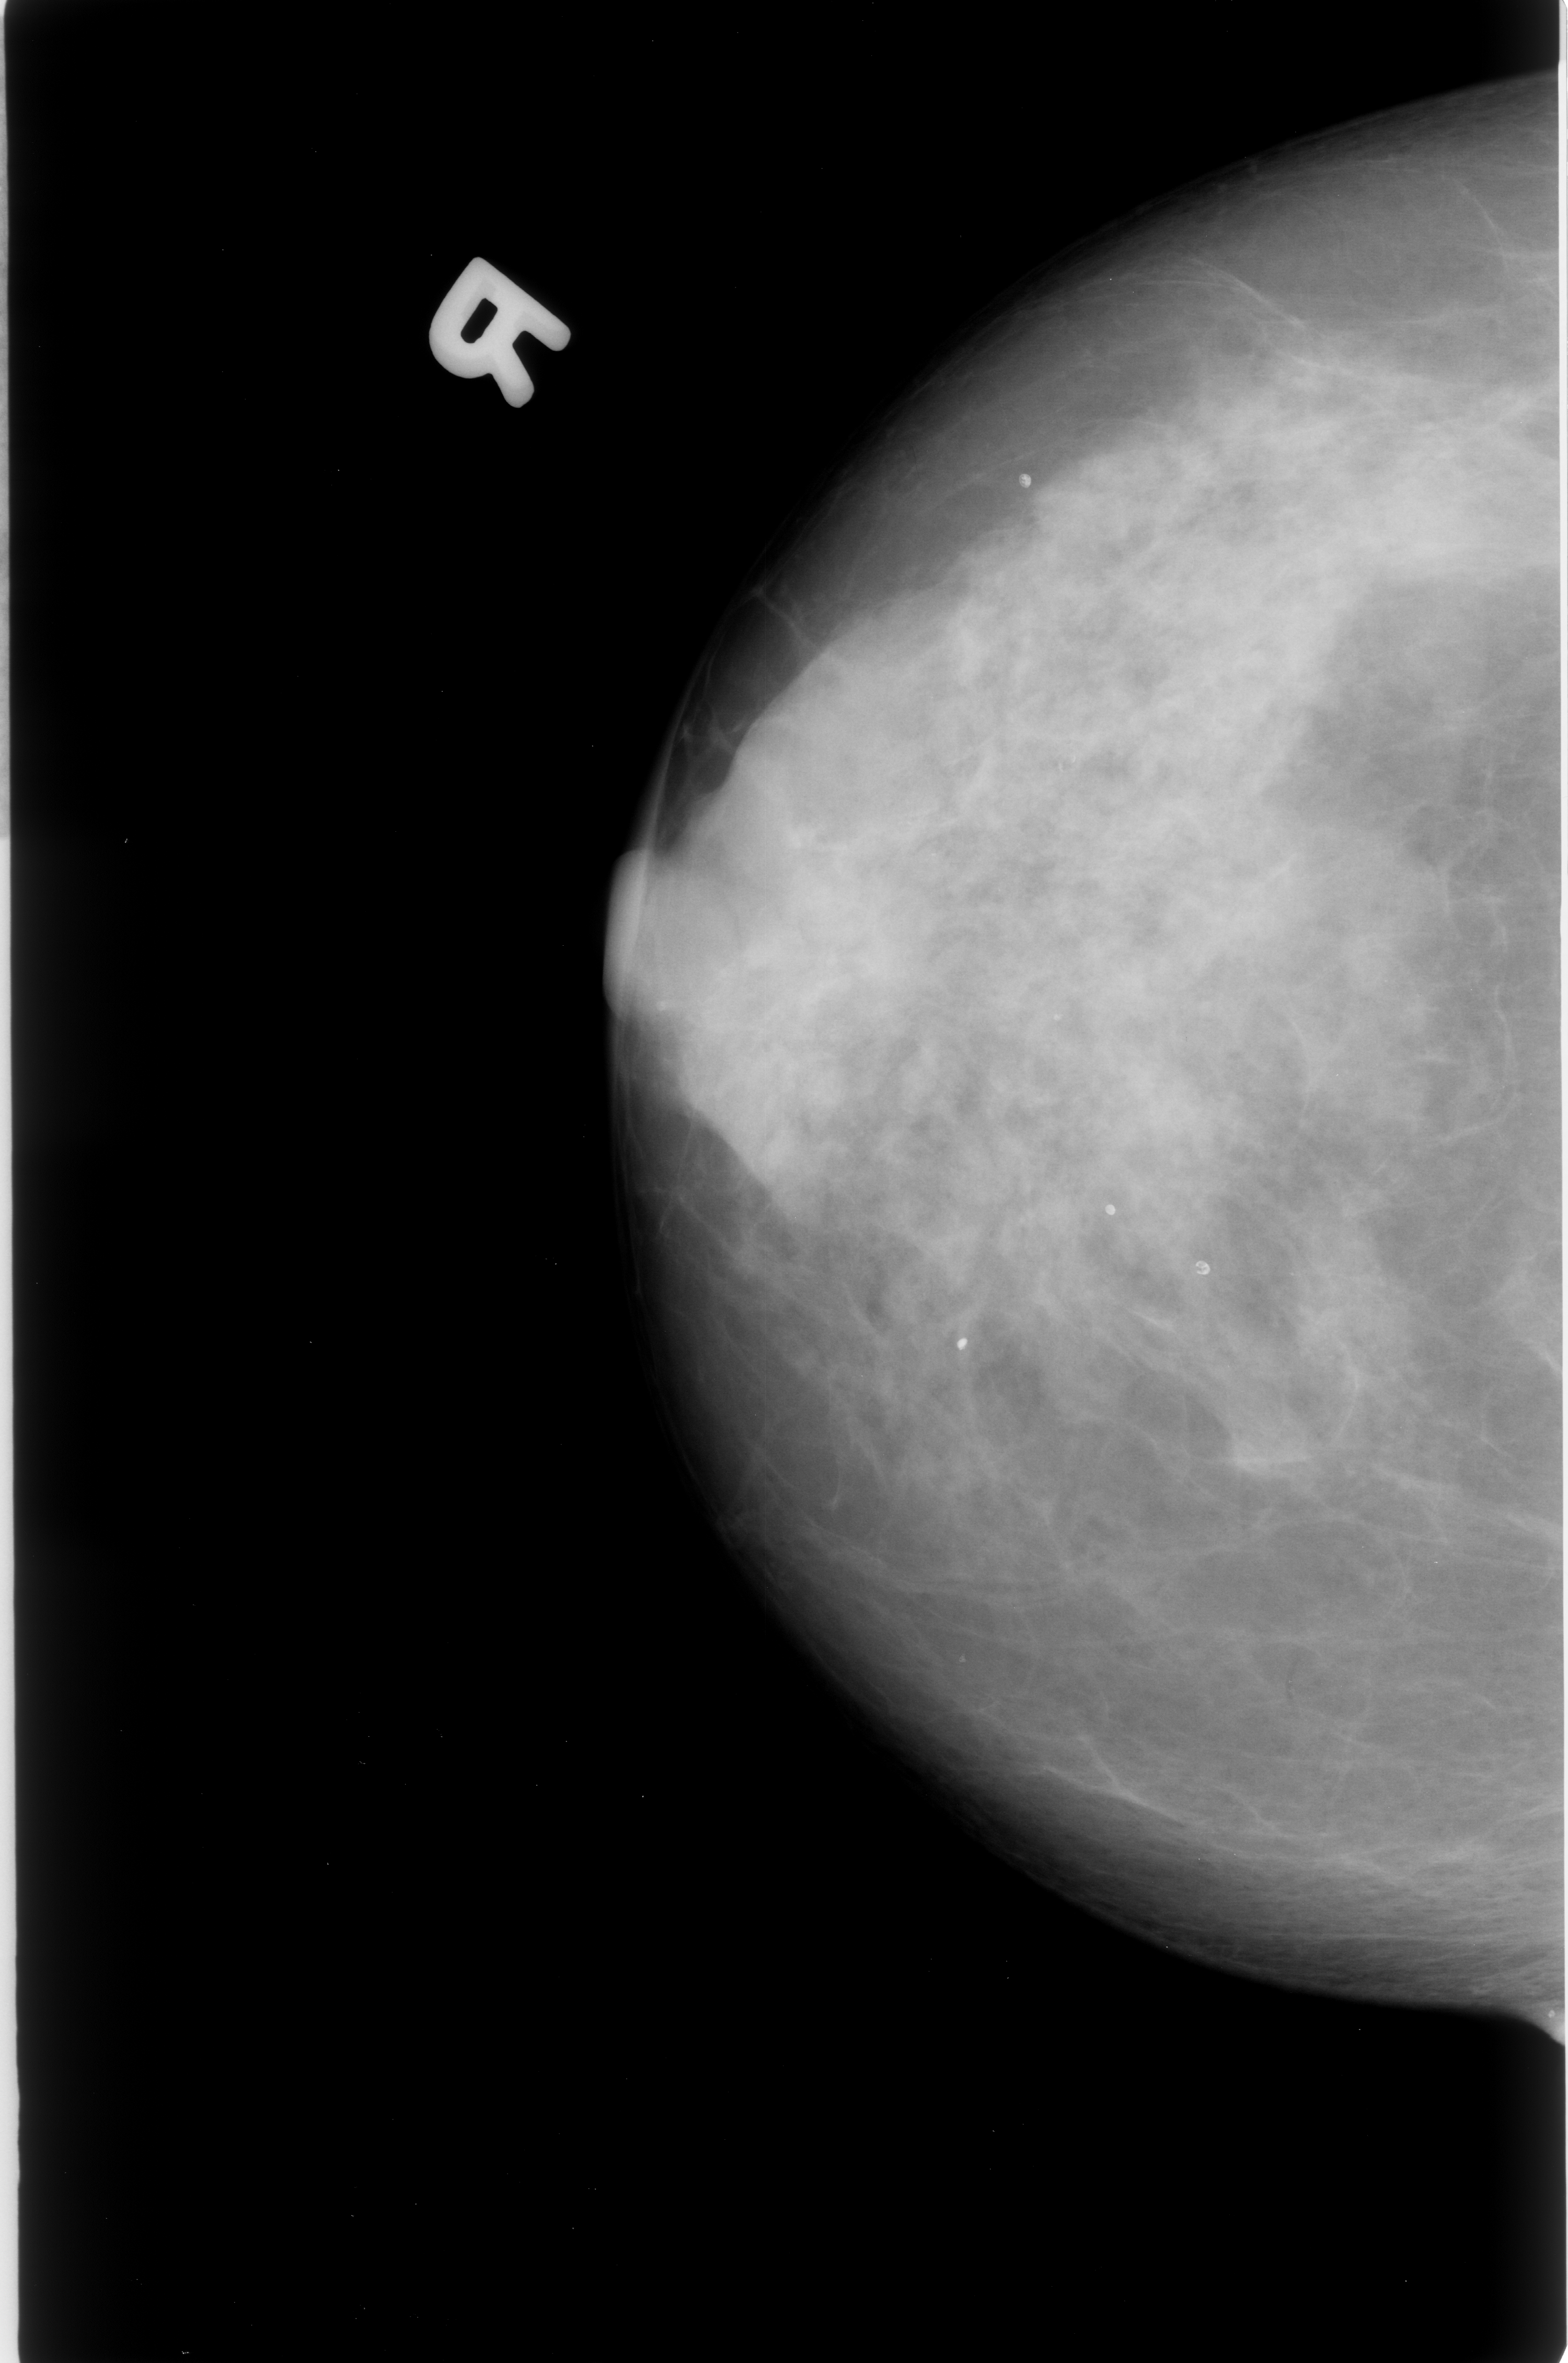
Digitized screen-film mammogram, right breast, CC view, BI-RADS breast density category 3 (scale 1–4).
Marked findings (only marked abnormalities are described; nothing is implied about the rest of the image): Finding 1 of 2: calcifications, morphology punctate / pleomorphic, distribution clustered; BI-RADS assessment category 3; subtlety rating 2 on a 1 (subtle) to 5 (obvious) scale; pathology (as recorded): malignant. Finding 2 of 2: calcifications, morphology punctate / pleomorphic, distribution clustered; BI-RADS assessment category 3; subtlety rating 2 on a 1 (subtle) to 5 (obvious) scale; pathology result (as recorded, not read from the image): malignant.